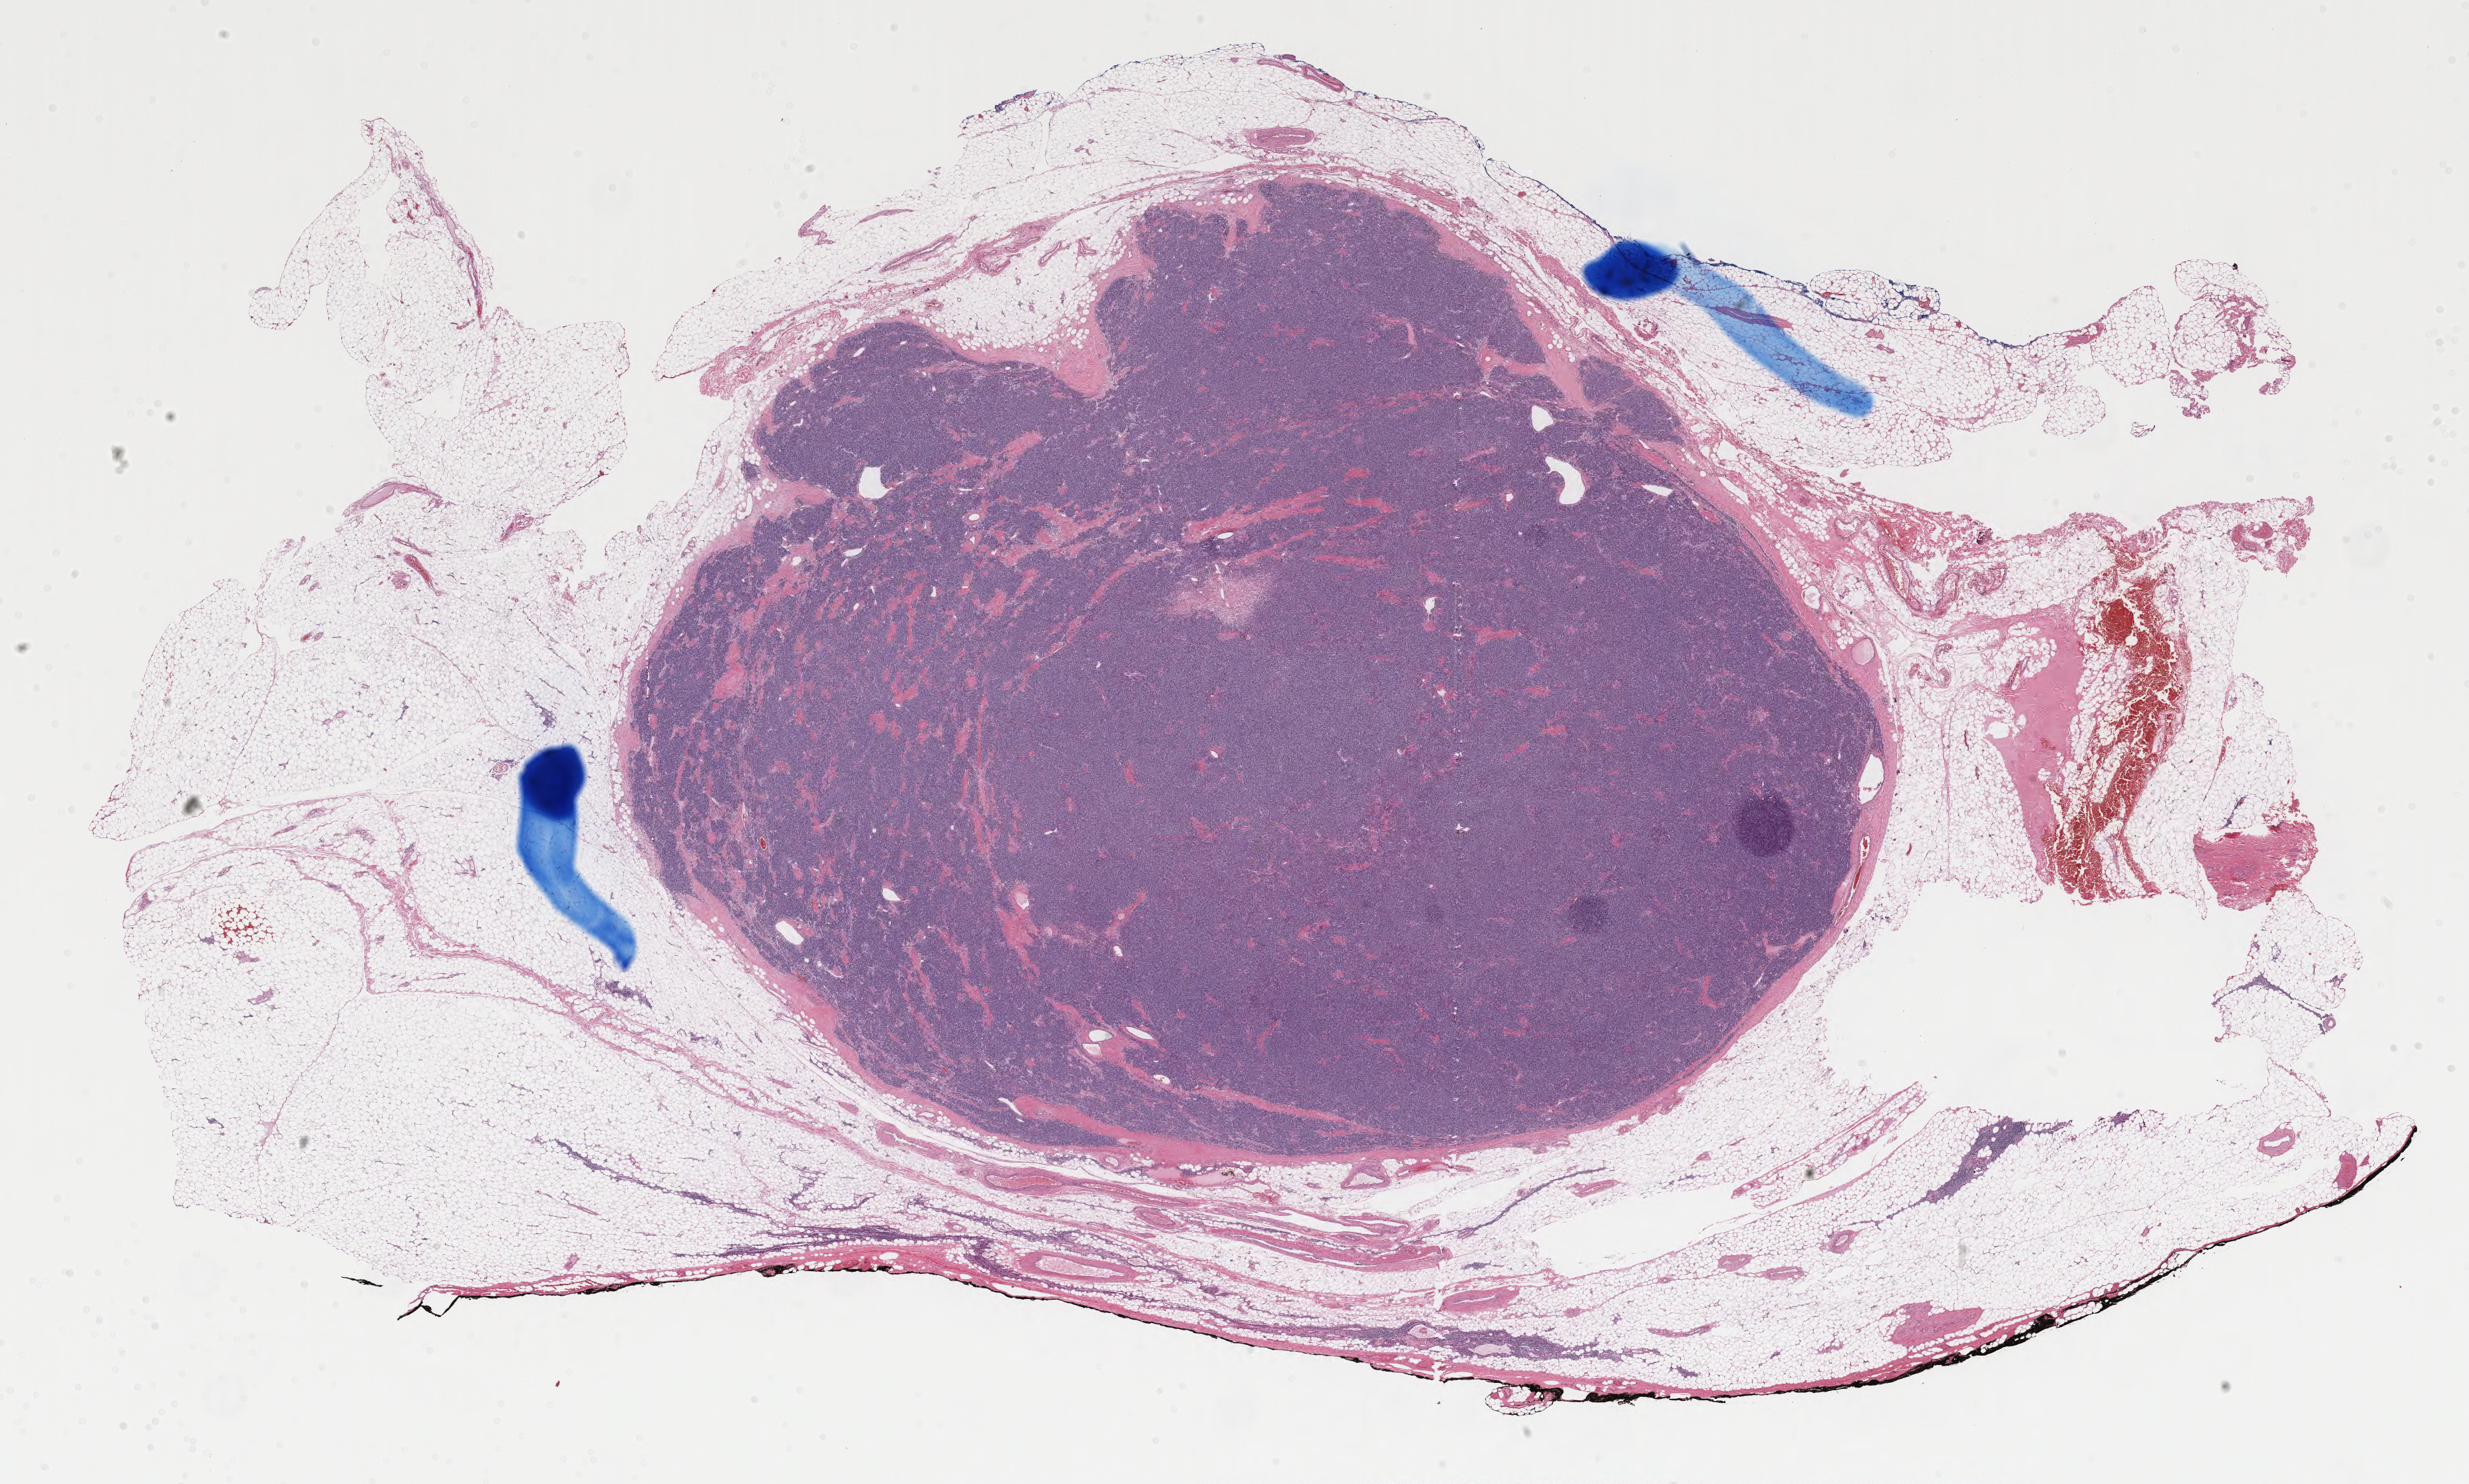
H&E-stained whole-slide image, a low-resolution overview of the entire scanned area, about 29.4 x 17.7 mm. Formalin-fixed paraffin-embedded (FFPE) diagnostic section. Sample: primary tumour, thymus. Male, age 52 years at initial diagnosis.
* pathologic diagnosis: Thymoma, type A, malignant